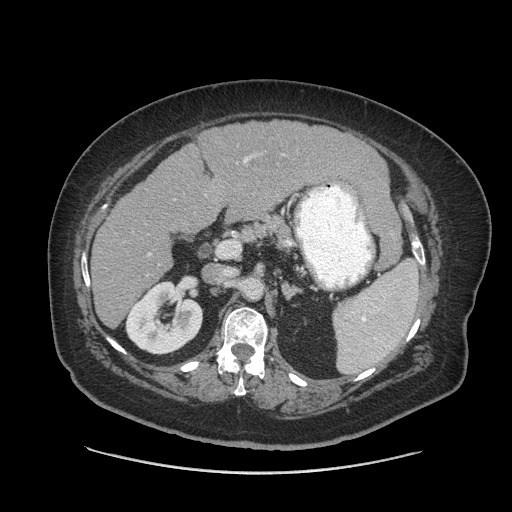
Contrast-enhanced abdominal CT (liver protocol), one axial slice. 140 kVp. Soft-tissue window (W 400 / L 40 HU). 2.5 mm slice thickness. 512 × 512 image matrix, field of view 420 × 420 mm. From the clinical record (not read from this slice): diagnosis: hepatocellular carcinoma (patient treated with transarterial chemoembolisation; whether this scan precedes or follows treatment is not stated here); TNM stage (as recorded): Stage-I; Child-Pugh class: A; tumour differentiation: well differentiated; tumour nodularity: uninodular.
Outlined on this slice (semi-automatically segmented with operator editing):
- liver parenchyma outside the tumour (the mass and vessels are separate outlines, so this box may not span the whole liver): bounding box (x1, y1, x2, y2) in pixels: (90, 120, 390, 327)
- liver vessels: (149, 157, 250, 255)